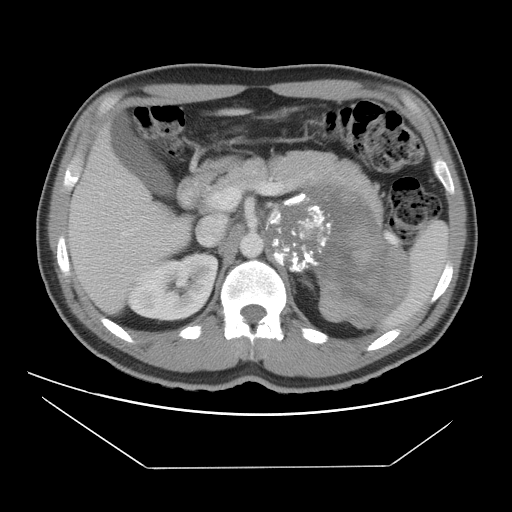
Contrast-enhanced abdominal CT, one axial slice; position 70 of 131 along the scan axis; reconstruction kernel STANDARD; 120 kVp; intravenous contrast given; soft-tissue window (W 400 / L 40 HU); 5 mm slice thickness; 512 × 512 image matrix, field of view 396 × 396 mm. Male patient, age 44 years. Case-level facts recorded for this patient, not image findings: diagnosis: adrenocortical carcinoma; tumour side: left adrenal; tumour size at pathology: 15.5 cm; Ki-67 index: 6 %; stage (as recorded): 2.
Outlined on this slice (semi-automatically segmented with operator editing):
- mass: bounding box (x1, y1, x2, y2) in pixels: (267, 185, 406, 325)